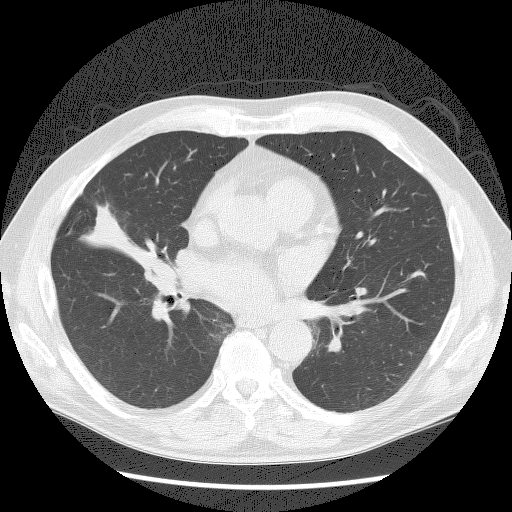
Chest CT (low-dose screening protocol), one axial image, third annual screen, lung window (W 1500 / L -600 HU), lung (sharp) reconstruction kernel (BONE), 120 kVp, slice 72 of 146 in the series. Male, age 57 years at enrolment.
Expert reader's lesion annotation, bounding box (x1, y1, x2, y2) in pixels: (141, 252, 179, 290). Reader record for this screening exam (exam-level; its link to the box is not recorded): non-calcified nodule or mass ≥4 mm, right middle lobe, 19 × 18 mm, smooth margins, soft tissue attenuation, pre-existing on the prior screen: yes; interval growth: yes. Official screen result: positive, other. Participant outcome: lung cancer diagnosed 69 days after this screen — carcinoid tumor, NOS, right middle lobe, carcinoid, stage not assessed, 15 mm at pathology.